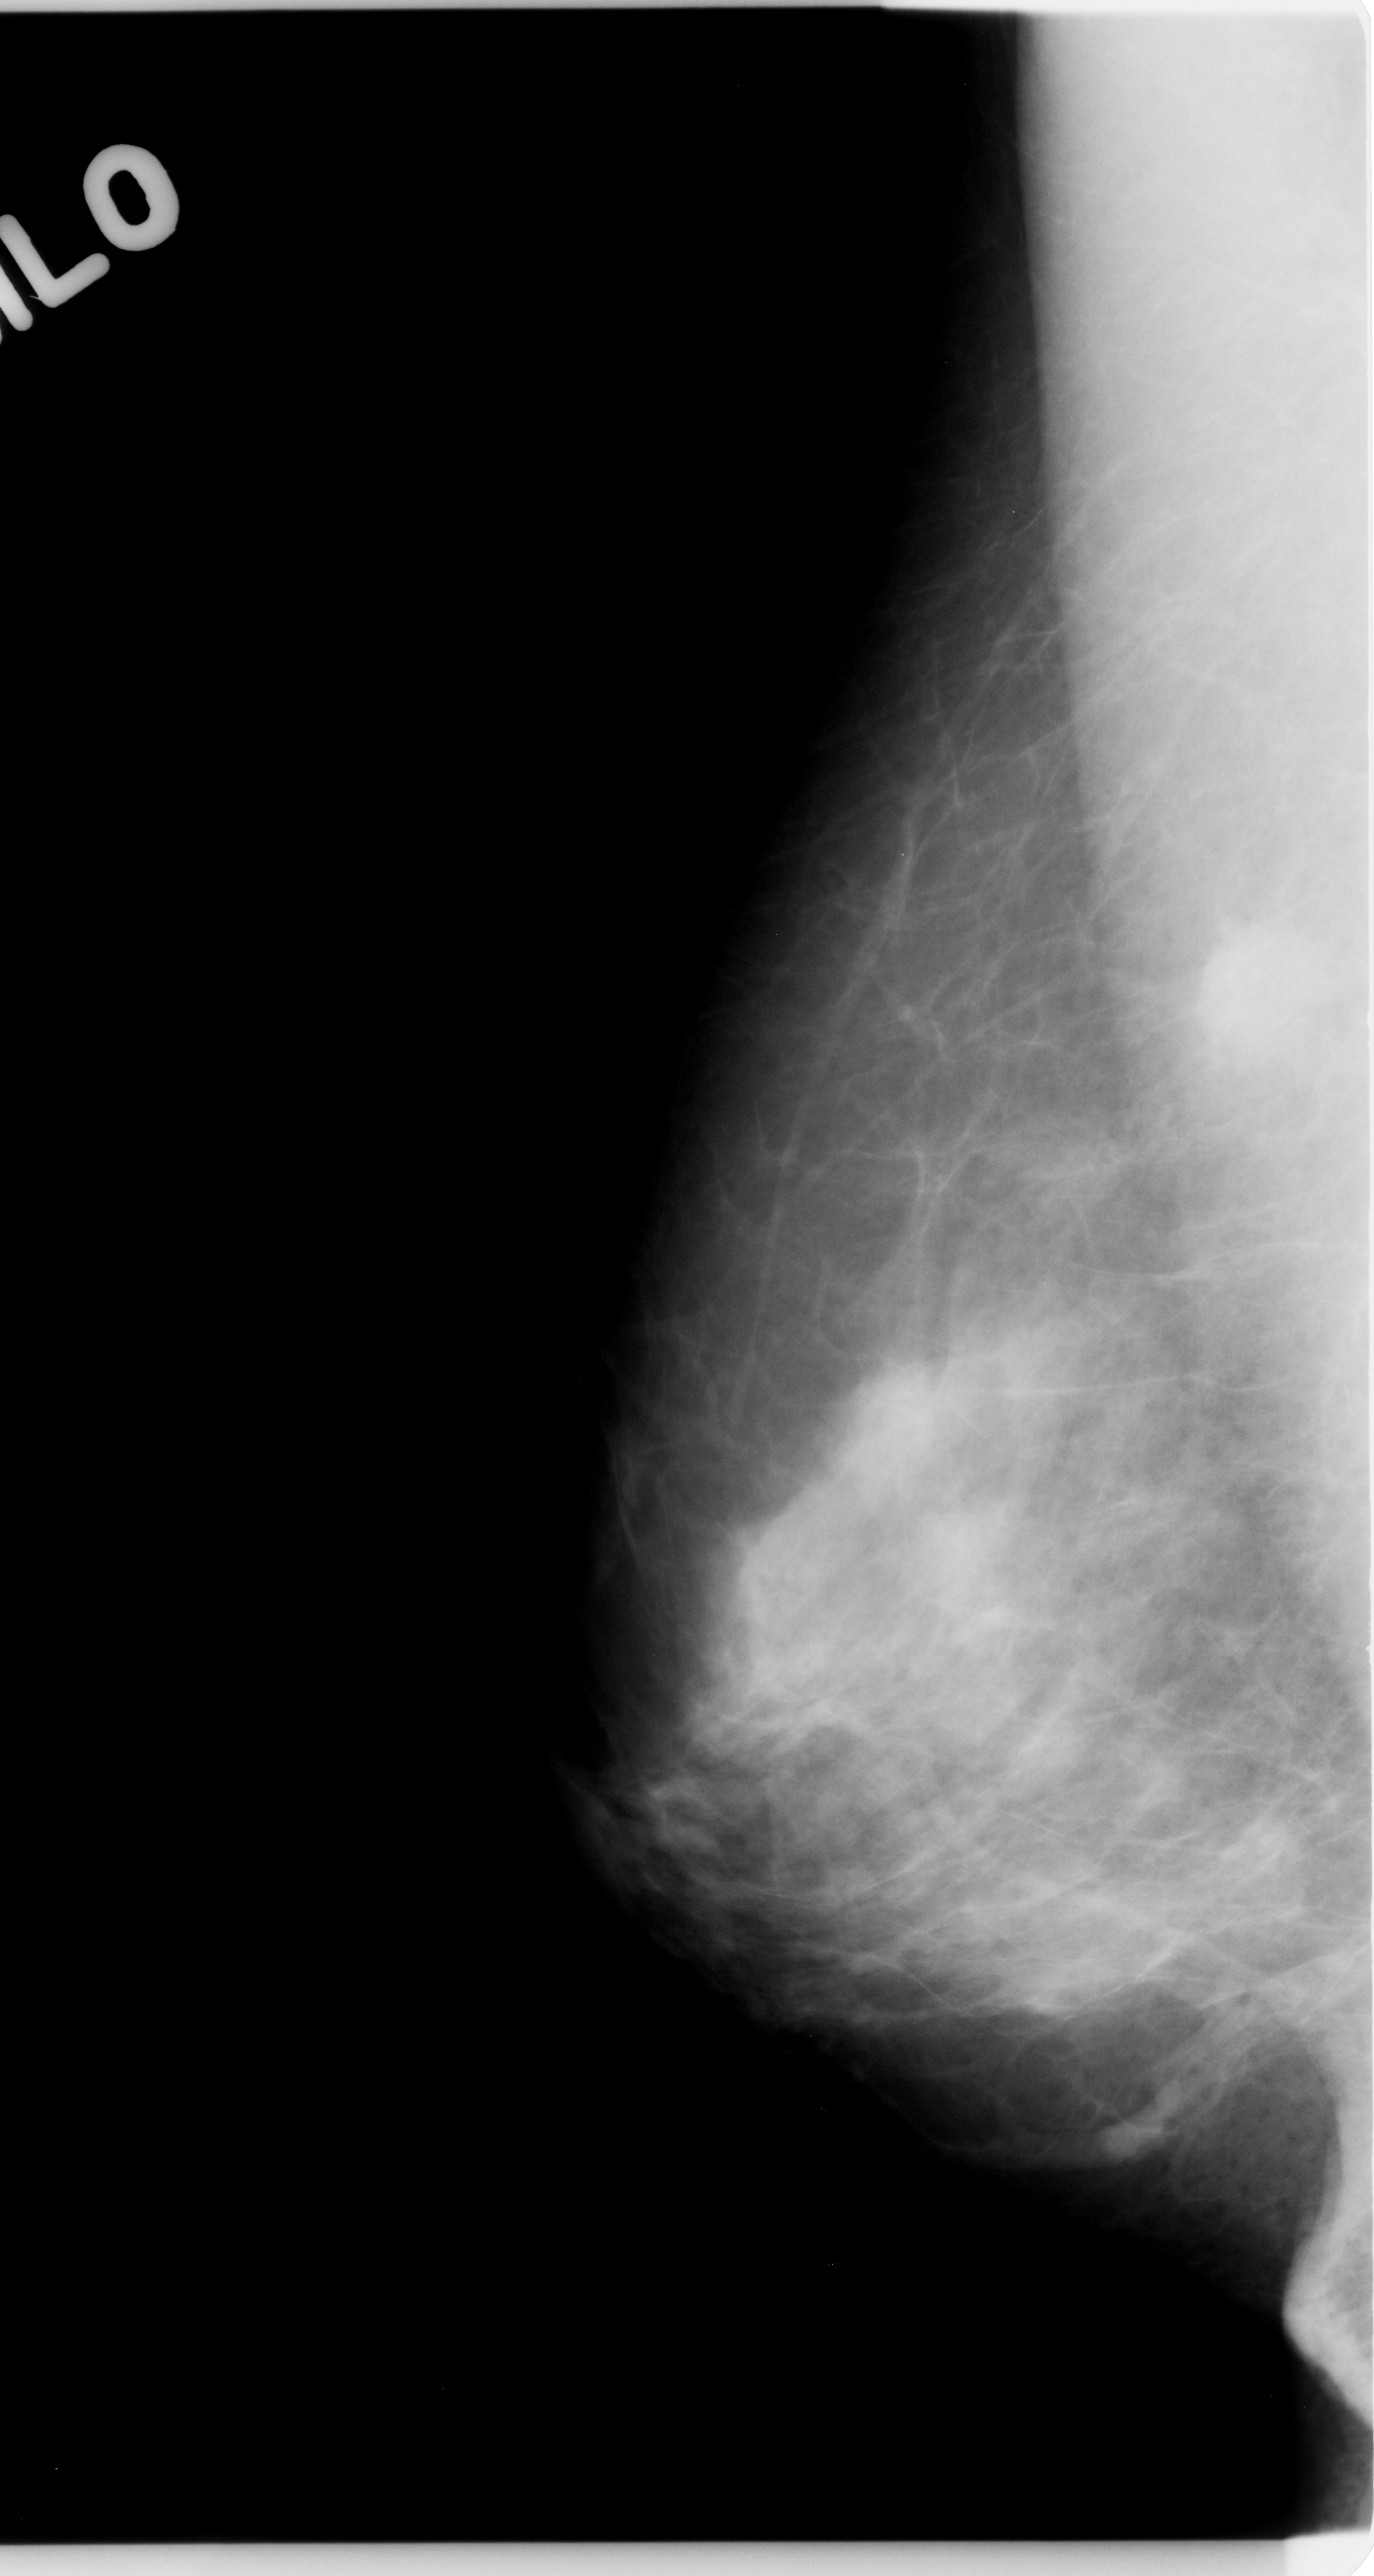
Digitized screen-film mammogram; right breast; MLO view; BI-RADS breast density category 2 (scale 1–4).
Marked abnormality: mass, shape round, margins spiculated; BI-RADS assessment category 5; subtlety rating 5 on a 1 (subtle) to 5 (obvious) scale; pathology result (as recorded, not read from the image): malignant.